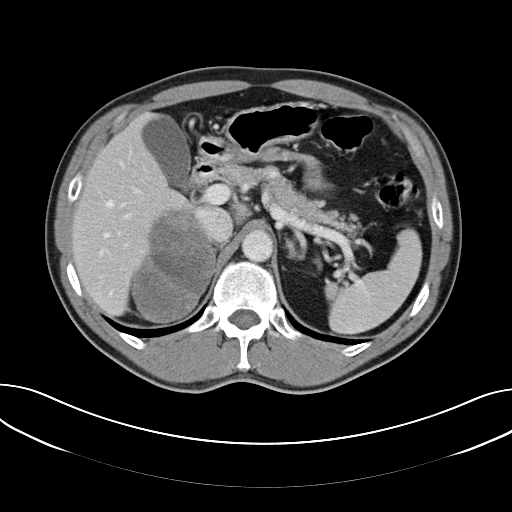
Contrast-enhanced abdominal CT, one axial slice; reconstruction kernel B40f; 120 kVp; intravenous contrast given; soft-tissue window (W 400 / L 40 HU); 5 mm slice thickness; 512 × 512 image matrix, field of view 372 × 372 mm. Patient: male, 57 years. Case-level facts recorded for this patient, not image findings: diagnosis: adrenocortical carcinoma; tumour side: right adrenal; tumour size at pathology: 11.2 cm; Ki-67 index: 10 %; stage (as recorded): 3.
Annotated regions visible in this slice (semi-automatic segmentation, software-assisted and operator-edited):
- mass: bounding box <133,211,213,322> (left, top, right, bottom; pixels)